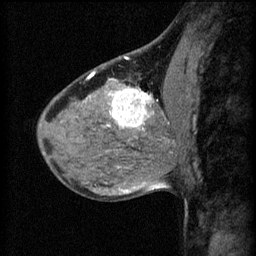
Breast MRI (dynamic contrast-enhanced), one sagittal slice; position 29 of 60 along the scan axis; 3 images stored at this slice position (order not interpretable as contrast timing); 1.5 T; TE 4.2 ms, TR 8.2 ms; 256 × 256 image matrix, field of view 180 × 180 mm. Female patient, age 40 years.
Structures marked on this image (semi-automatic segmentation, software-assisted and operator-edited):
- analysis volume of interest (the breast-tissue region the enhancement analysis was run in; not a lesion): box from (x=108, y=82) to (x=175, y=139) px
- tumour enhancement mask (voxels above the 70 % enhancement threshold inside the analysis volume of interest): (x=108, y=82)–(x=169, y=131)